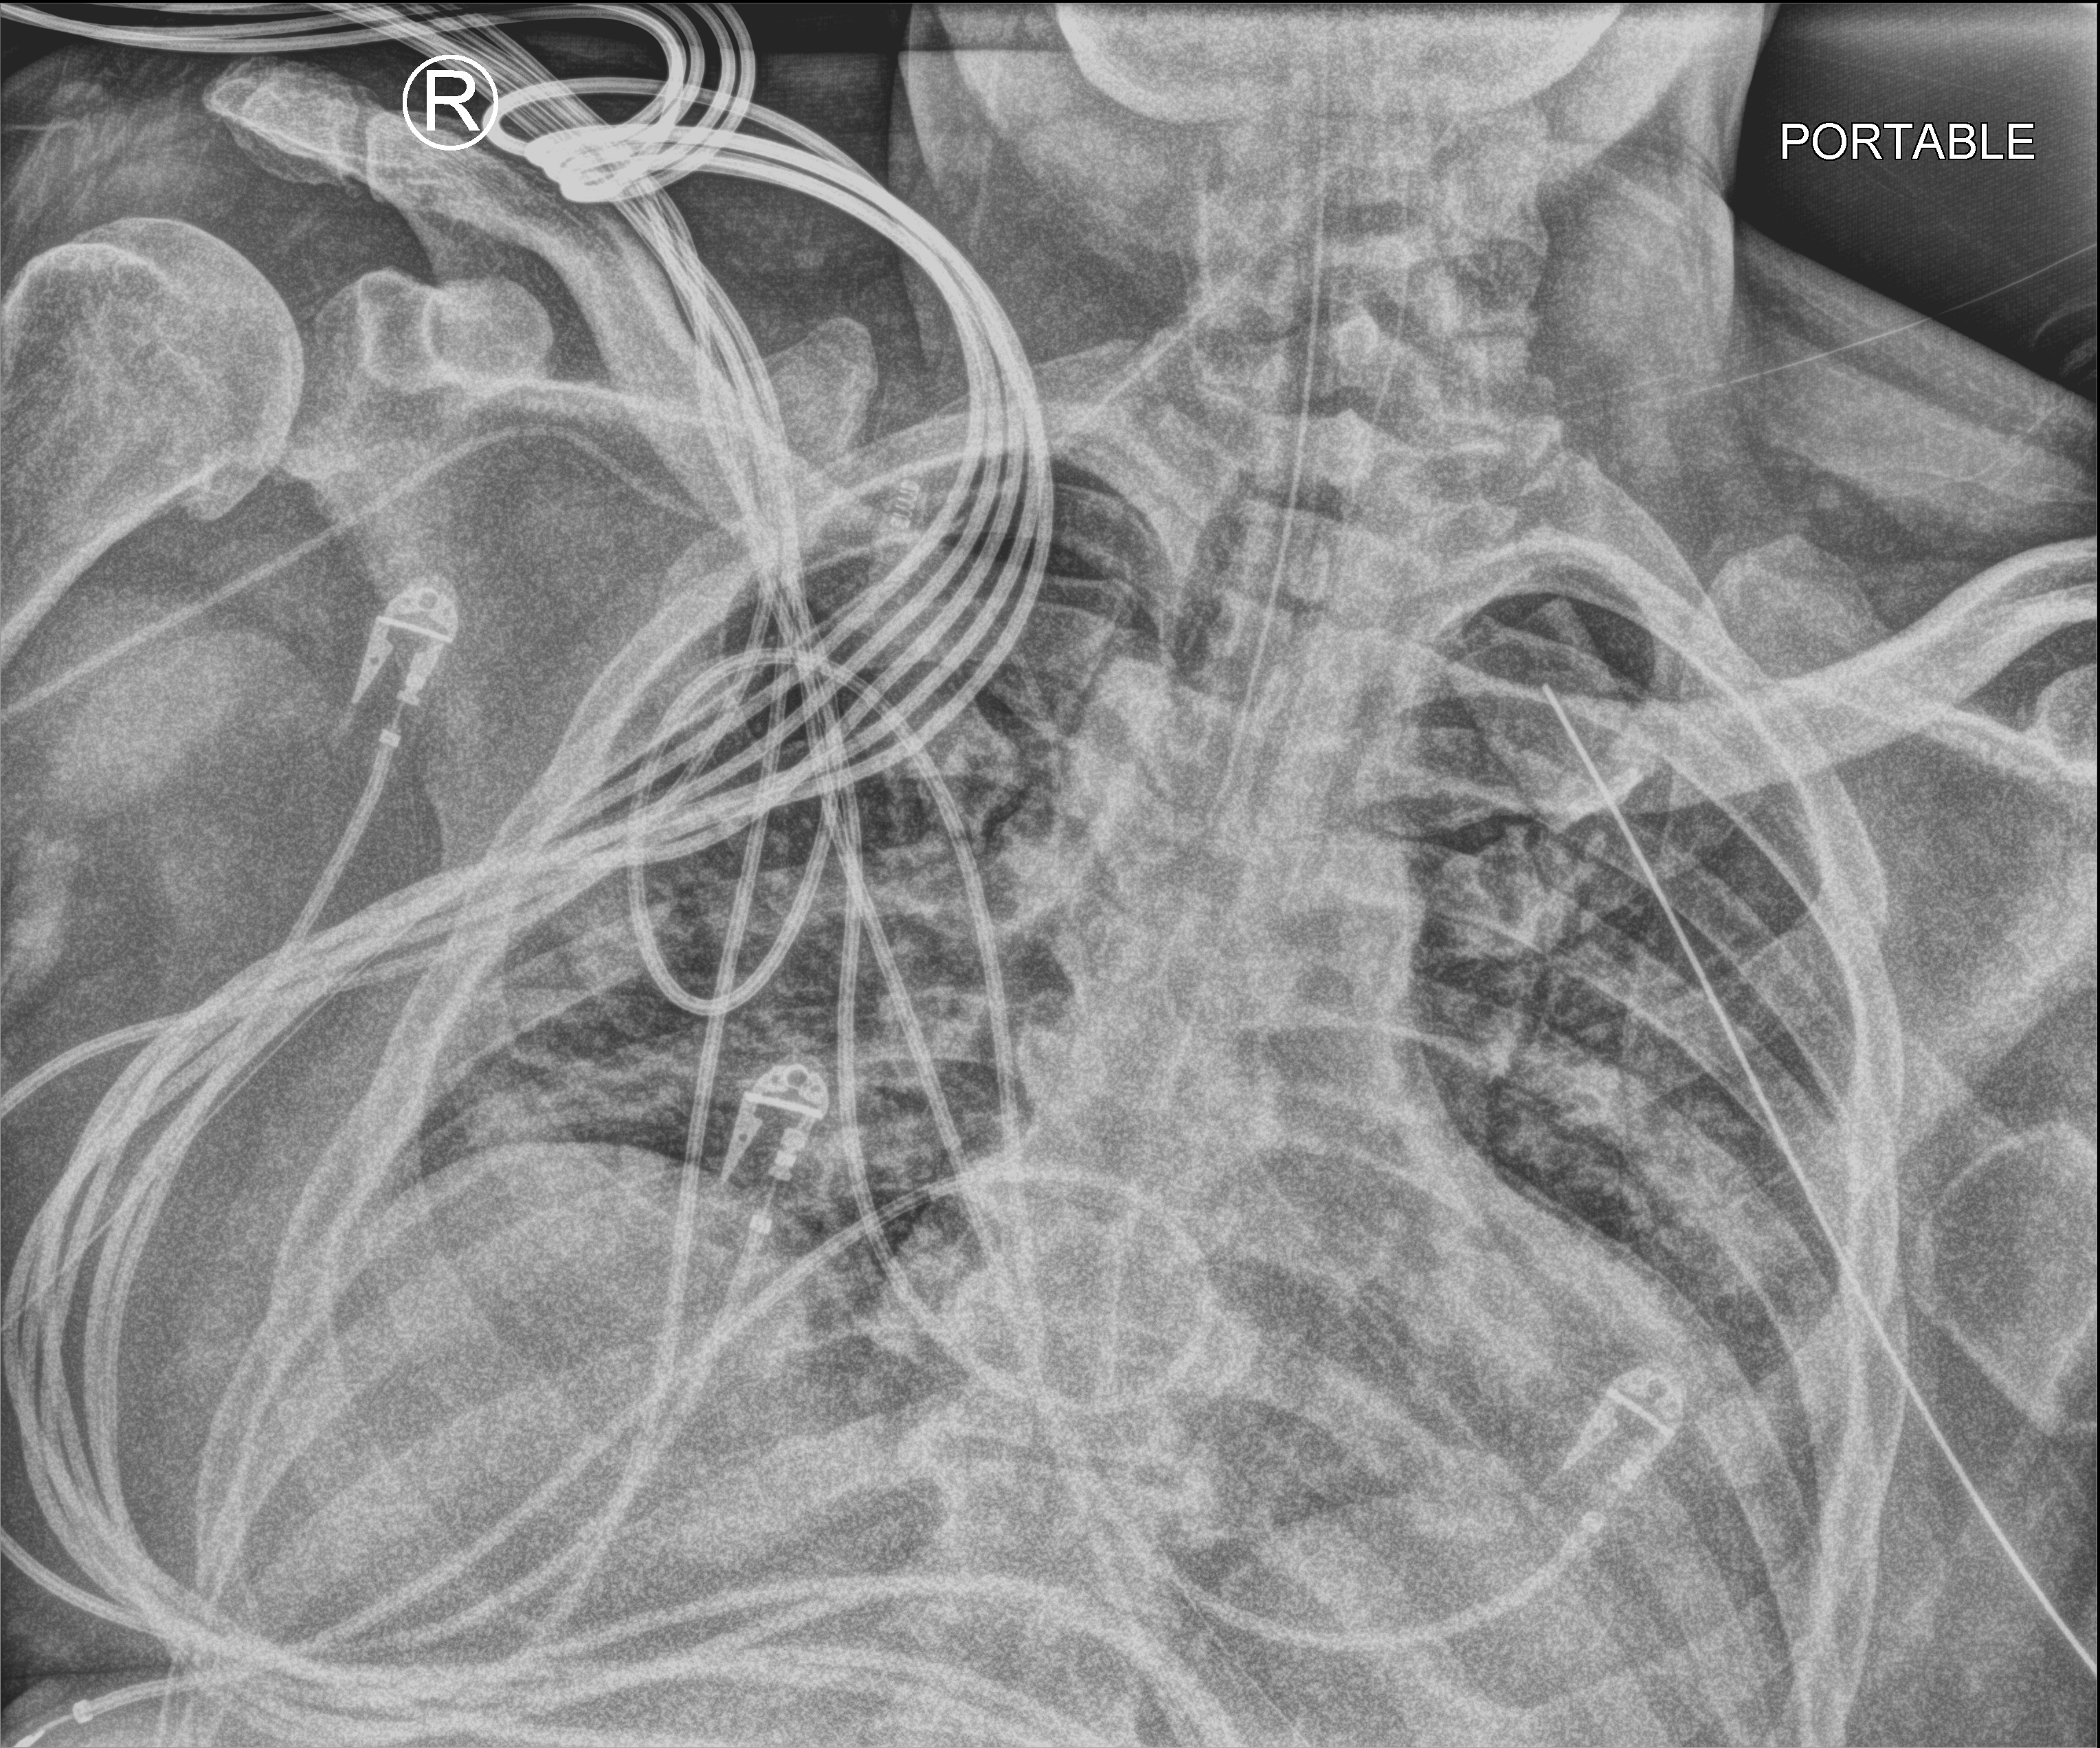
Portable chest radiograph; anteroposterior (AP) projection. Male patient hospitalised with COVID-19, age 18–59 years.
Admission-level facts for this patient (not findings on this image; timing relative to this image not recorded): chronic kidney disease (admission record): no; mechanically ventilated during this hospital stay: yes; length of hospital stay: 41 days.